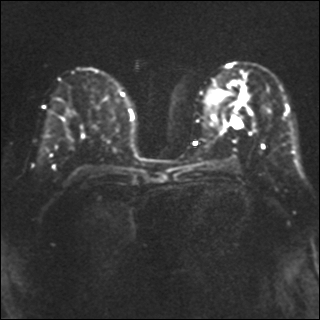
Breast MRI, one axial slice. Slice 18 of 40 in the series (ordered by position). Diffusion-weighted series; image 2 of 4 stored at this slice position (different b-values; order by instance number). 1.5 T. 4 mm slice thickness. 320 × 320 image matrix, field of view 320 × 320 mm. Female patient.
Annotated regions visible in this slice (manually delineated by an expert):
- tumour on diffusion-weighted imaging: bounding box [x1, y1, x2, y2] px = [230, 115, 243, 128]